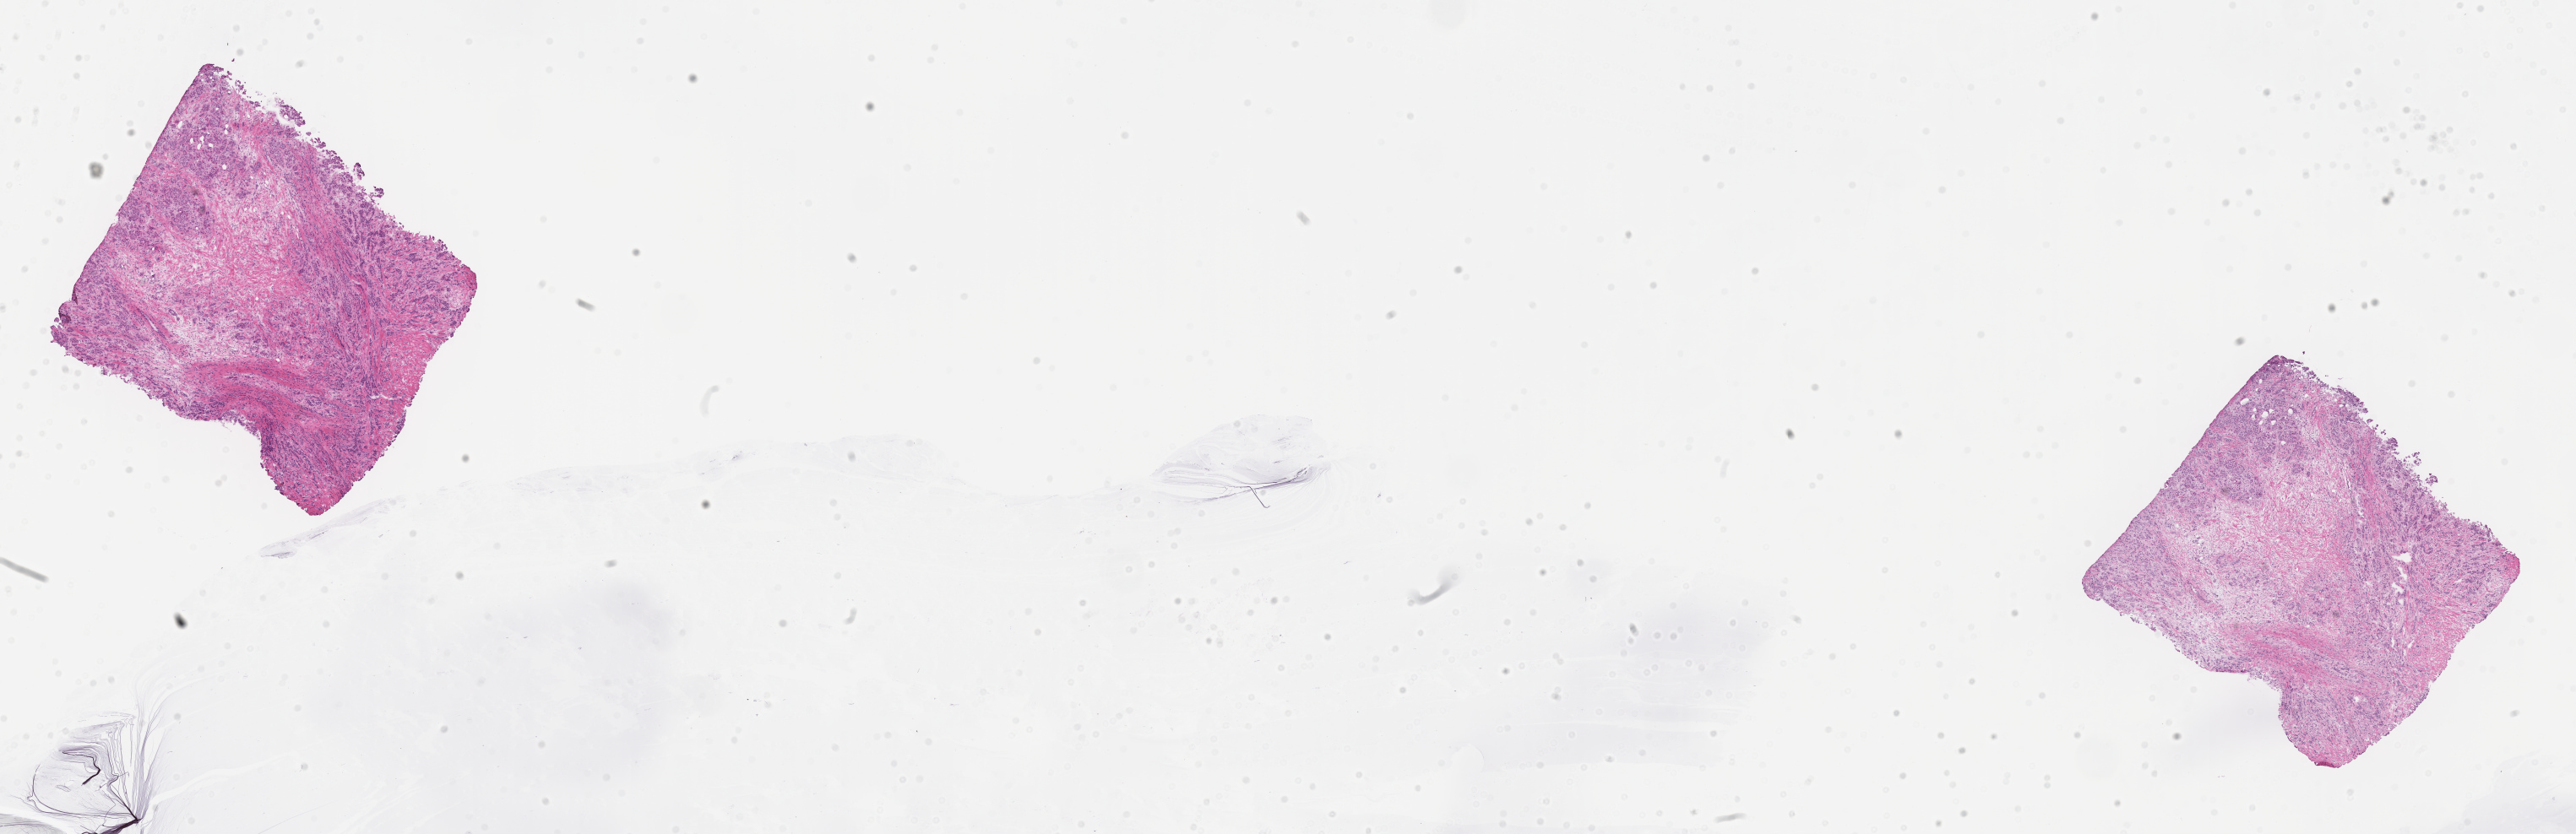
Whole-slide image, hematoxylin and eosin (H&E) stain — whole scanned area (about 24.6 x 8.0 mm) shown as a low-resolution overview. Frozen section. Specimen: primary tumor. Anatomic site: breast (right). Female, age 61 years at initial diagnosis. Composition of this section per pathologist review: tumor cells 80%, tumor nuclei 80%, stromal cells 20%, necrosis 0%, normal cells 0%. Infiltration values recorded for this section: lymphocyte infiltration 5%, monocyte infiltration 2%, neutrophil infiltration 6%.
Section: top of the tissue portion. Histologic diagnosis: Infiltrating duct carcinoma, NOS.